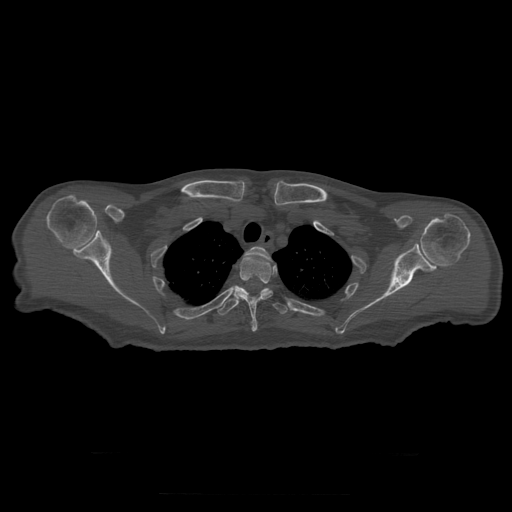
CT including the spine, one axial slice. Position 255 of 397 along the scan axis. 120 kVp. Bone window (W 1800 / L 400 HU). 512 × 512 image matrix, field of view 510 × 510 mm. Patient age 73 years. From the clinical record (not read from this slice): primary cancer: prostate.
Annotated regions visible in this slice (semi-automatically segmented with operator editing):
- T2 vertebra: bounding box (x1, y1, x2, y2) in pixels: (244, 247, 272, 261)
- T3 vertebra: (234, 255, 275, 332)
- T4 vertebra: (218, 288, 288, 316)